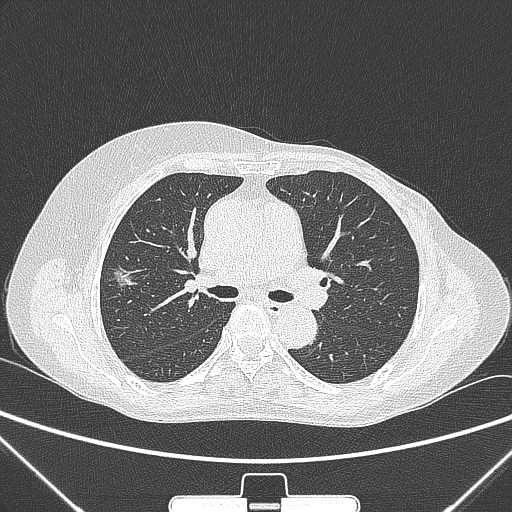
Chest CT, one axial slice; position 155 of 265 along the scan axis; 120 kVp; lung window (W 1500 / L -600 HU); 1 mm slice thickness; 512 × 512 image matrix, field of view 350 × 350 mm. Female patient, age 64 years. Case-level facts recorded for this patient, not image findings: clinical TNM (as recorded): T1c N0 M0; histopathological grade: G1-2.
Annotated regions visible in this slice (rectangle marked by the reading radiologist):
- lung tumour (recorded histology: adenocarcinoma): box from (x=106, y=259) to (x=139, y=296) px